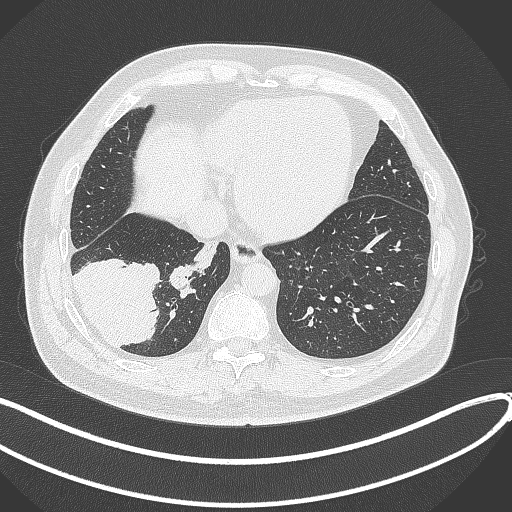
Chest CT, one axial slice. Slice 94 of 360 in the series (ordered by position). Reconstruction kernel B70f. 120 kVp. Lung window (W 1500 / L -600 HU). 512 × 512 image matrix. Patient: male, 59 years.
Outlined on this slice (bounding box drawn by a radiologist):
- lung tumour (recorded histology: adenocarcinoma): bounding box [x1, y1, x2, y2] px = [72, 252, 162, 348]